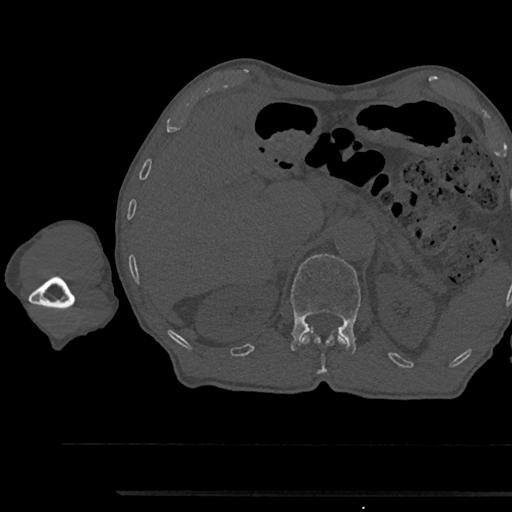
CT including the spine, one axial slice; slice 669 of 797 in the series (ordered by position); reconstruction kernel Br40s/3; 120 kVp; bone window (W 1800 / L 400 HU); 0.5 mm slice thickness; 512 × 512 image matrix, field of view 367 × 367 mm. Male patient, age 79 years. Case-level facts recorded for this patient, not image findings: primary cancer: prostate.
Structures marked on this image (semi-automatic segmentation, software-assisted and operator-edited):
- L1 vertebra: bounding box <291,254,361,354> (left, top, right, bottom; pixels)
- T12 vertebra: <301,332,349,374>